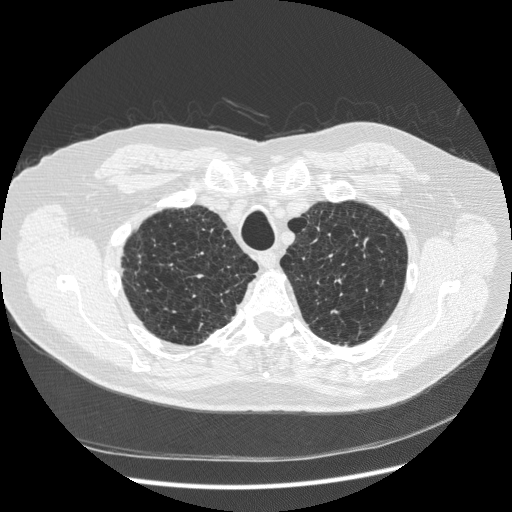
Axial slice from a low-dose chest CT screening exam. First (baseline) screen. Lung window (W 1500 / L -600 HU). 1.25 mm slice thickness. Standard (soft-tissue) reconstruction kernel (STANDARD). Slice 46 of 265 in the series. 512 × 512 image matrix, field of view 380 × 380 mm. Male participant, aged 70 years at enrolment.
Expert-annotated lung lesion, bounding box <331,216,385,270> (left, top, right, bottom; pixels). The screening reader recorded 2 non-calcified nodules or masses ≥4 mm on this exam; which of them this box marks is not recorded. Official screen result: positive, change unspecified: nodule(s) >= 4 mm or enlarging nodule(s), mass(es), or other non-specific abnormalities suspicious for lung cancer. Lung cancer was diagnosed 816 days after this screen (after the third annual screen): squamous cell carcinoma, NOS, left upper lobe, moderately differentiated (G2), stage IA (AJCC 6th edition), 18 mm at pathology.